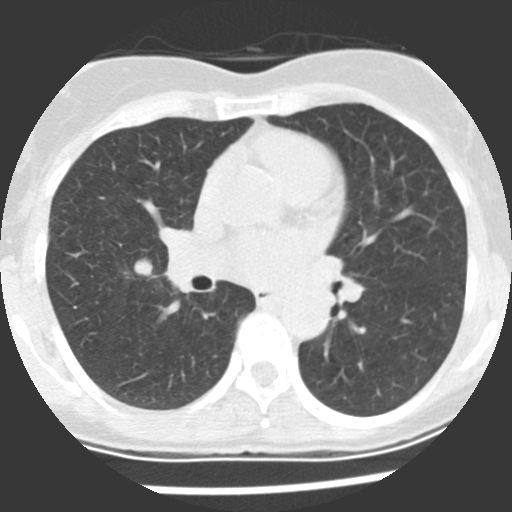
Axial slice from a low-dose chest CT screening exam. First (baseline) screen. Lung window (W 1500 / L -600 HU). Standard (soft-tissue) reconstruction kernel (STANDARD). Slice 108 of 225 in the series. Female, age 60 years at enrolment. Current smoker at enrolment.
Lesion marked by an expert reader, bounding box [x1, y1, x2, y2] px = [116, 250, 175, 295]. The screening reader recorded 2 non-calcified nodules or masses ≥4 mm on this exam (right upper lobe, right middle lobe); which of them this box marks is not recorded. Official screen result: positive, change unspecified: nodule(s) >= 4 mm or enlarging nodule(s), mass(es), or other non-specific abnormalities suspicious for lung cancer.